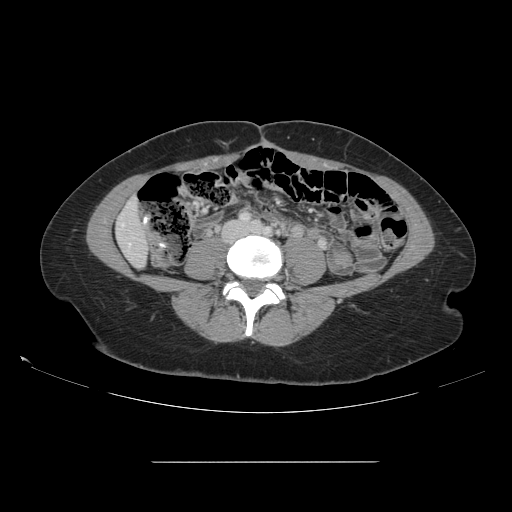
Contrast-enhanced abdominal CT, one axial slice. 120 kVp. Intravenous contrast given. Soft-tissue window (W 400 / L 40 HU). 2.5 mm slice thickness. 512 × 512 image matrix. Female patient, age 46 years. From the clinical record (not read from this slice): diagnosis: colorectal cancer liver metastases, imaged before liver resection; multiple liver metastases: yes; largest metastasis: 3 cm.
Annotated regions visible in this slice (outlined manually by an expert reader):
- liver: bounding box <117,201,149,267> (left, top, right, bottom; pixels)
- planned liver remnant (the part of the liver to remain after resection): <117,201,149,266>